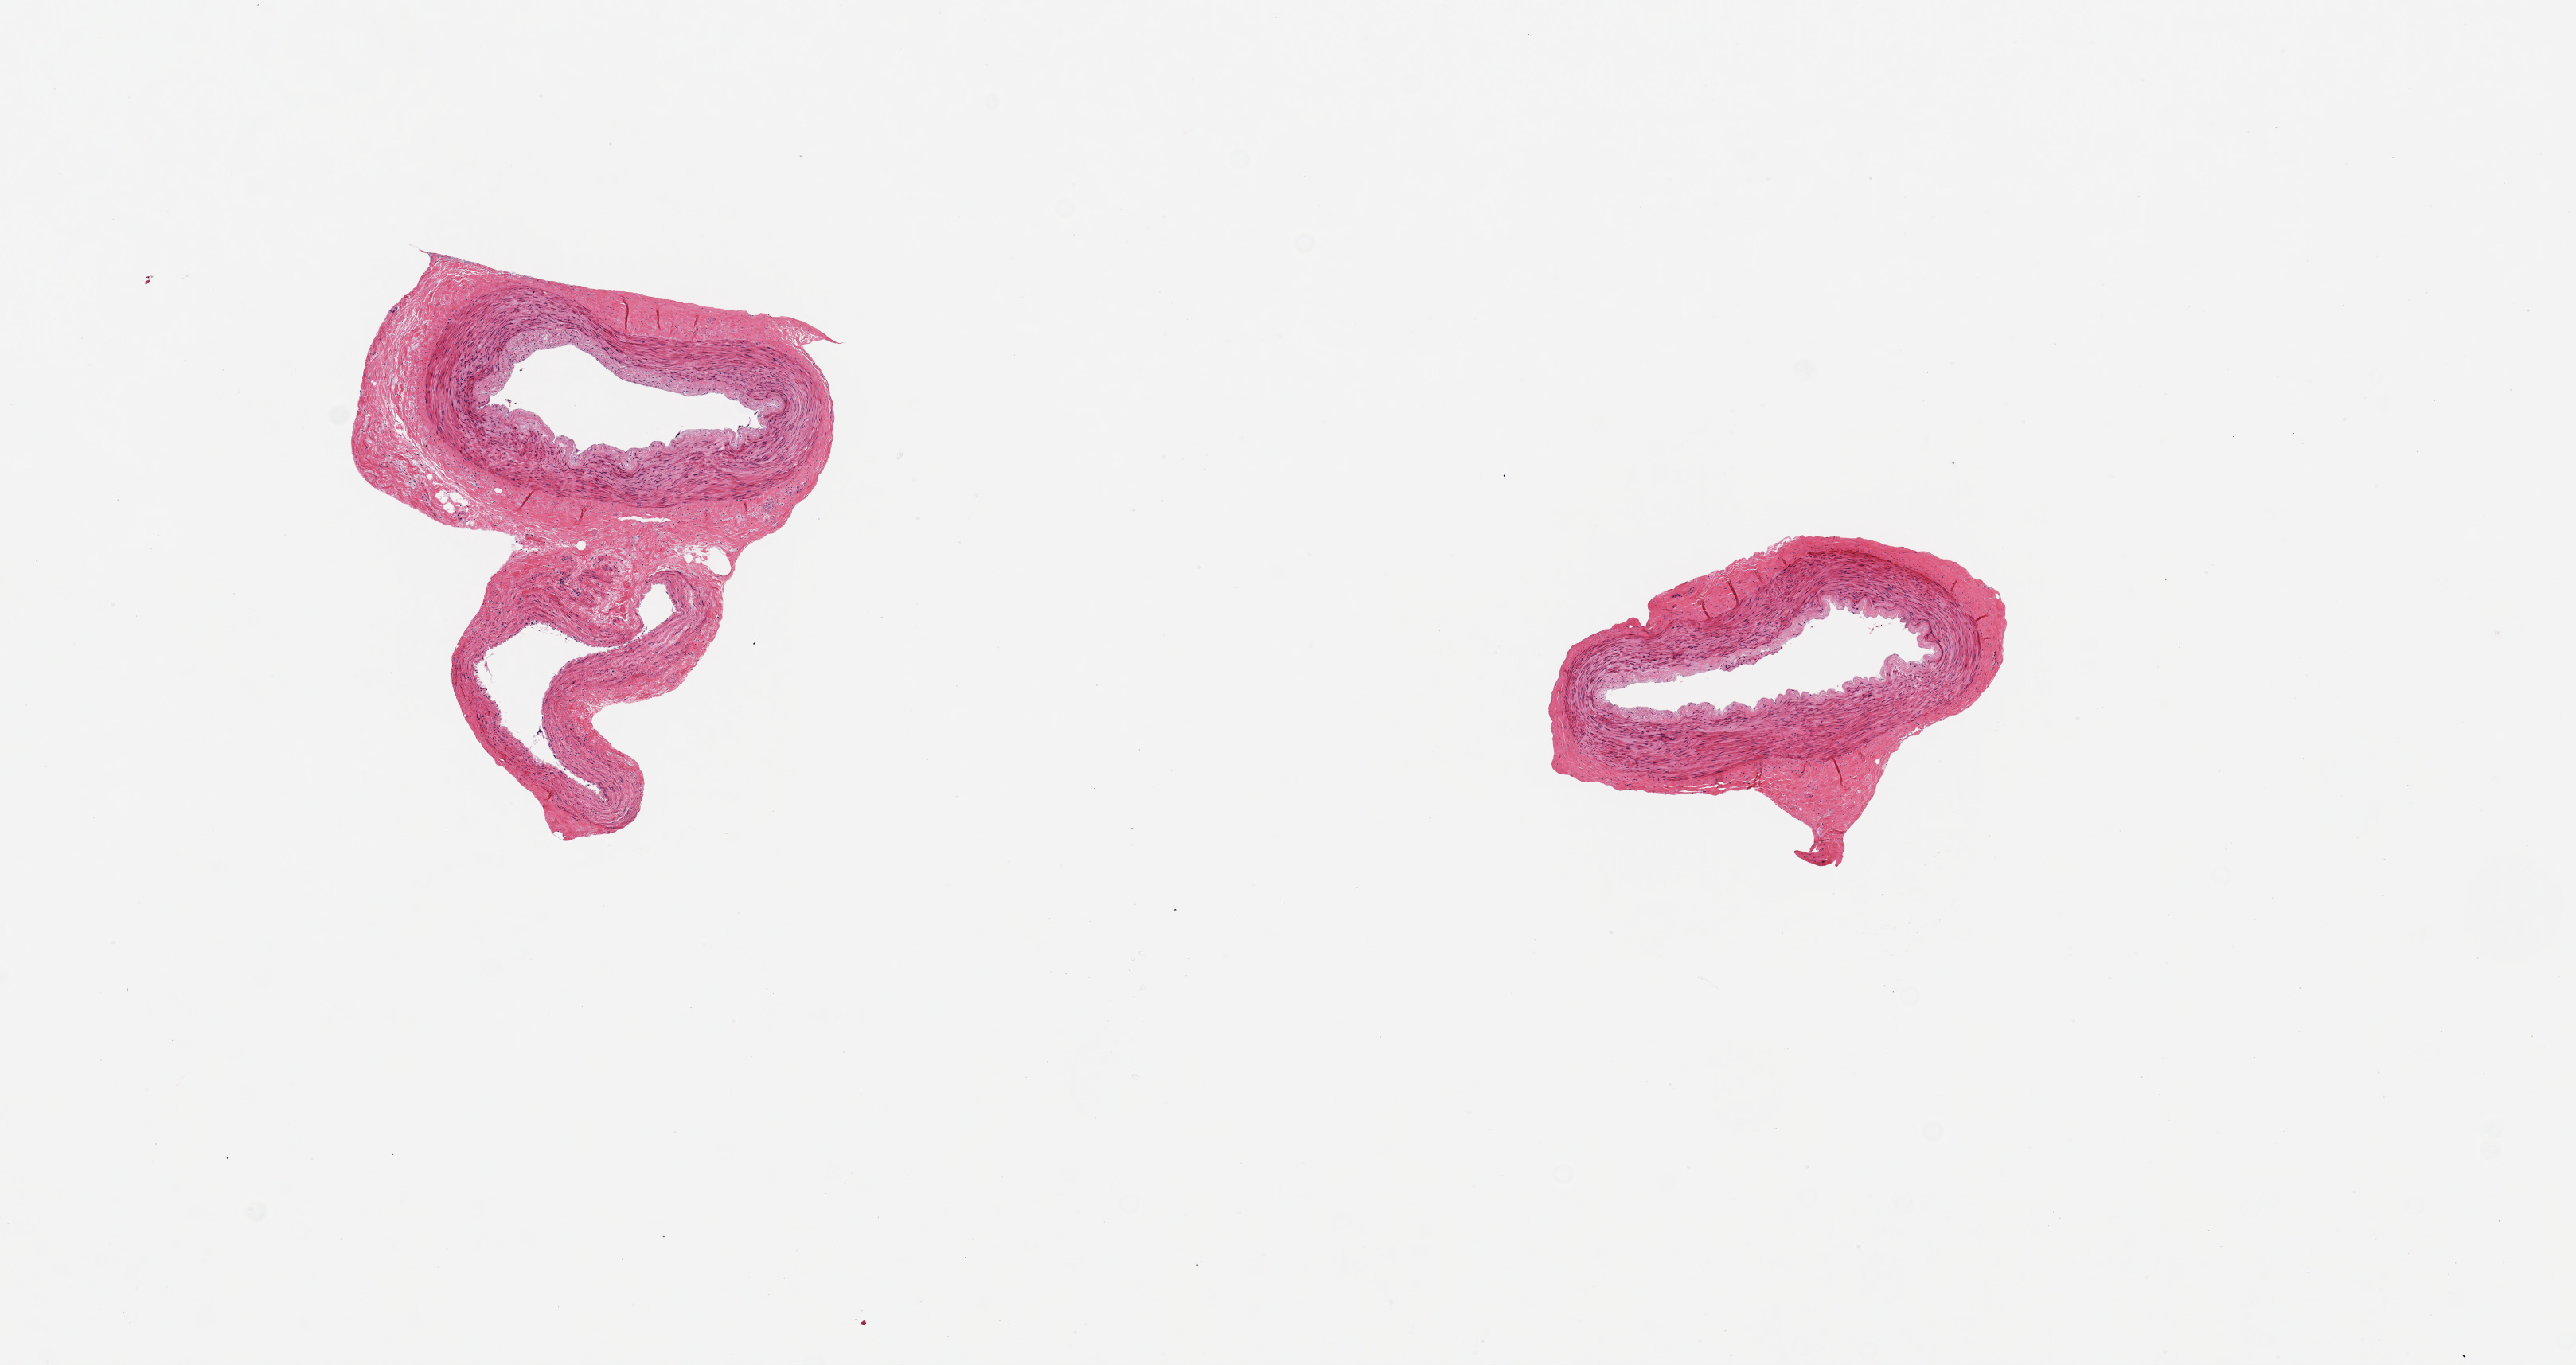
Digitized H&E-stained section, whole scanned area (about 12.8 x 6.8 mm, from a 20x scan) shown as a low-resolution overview. PAXgene-fixed paraffin-embedded (PFPE) section. Section of tibial artery (target tissue). Donor tissue sample. Donor: male.
Pathologist's review note for this sample: 2 pieces, 3x2 & 2x2mm; no lesions.